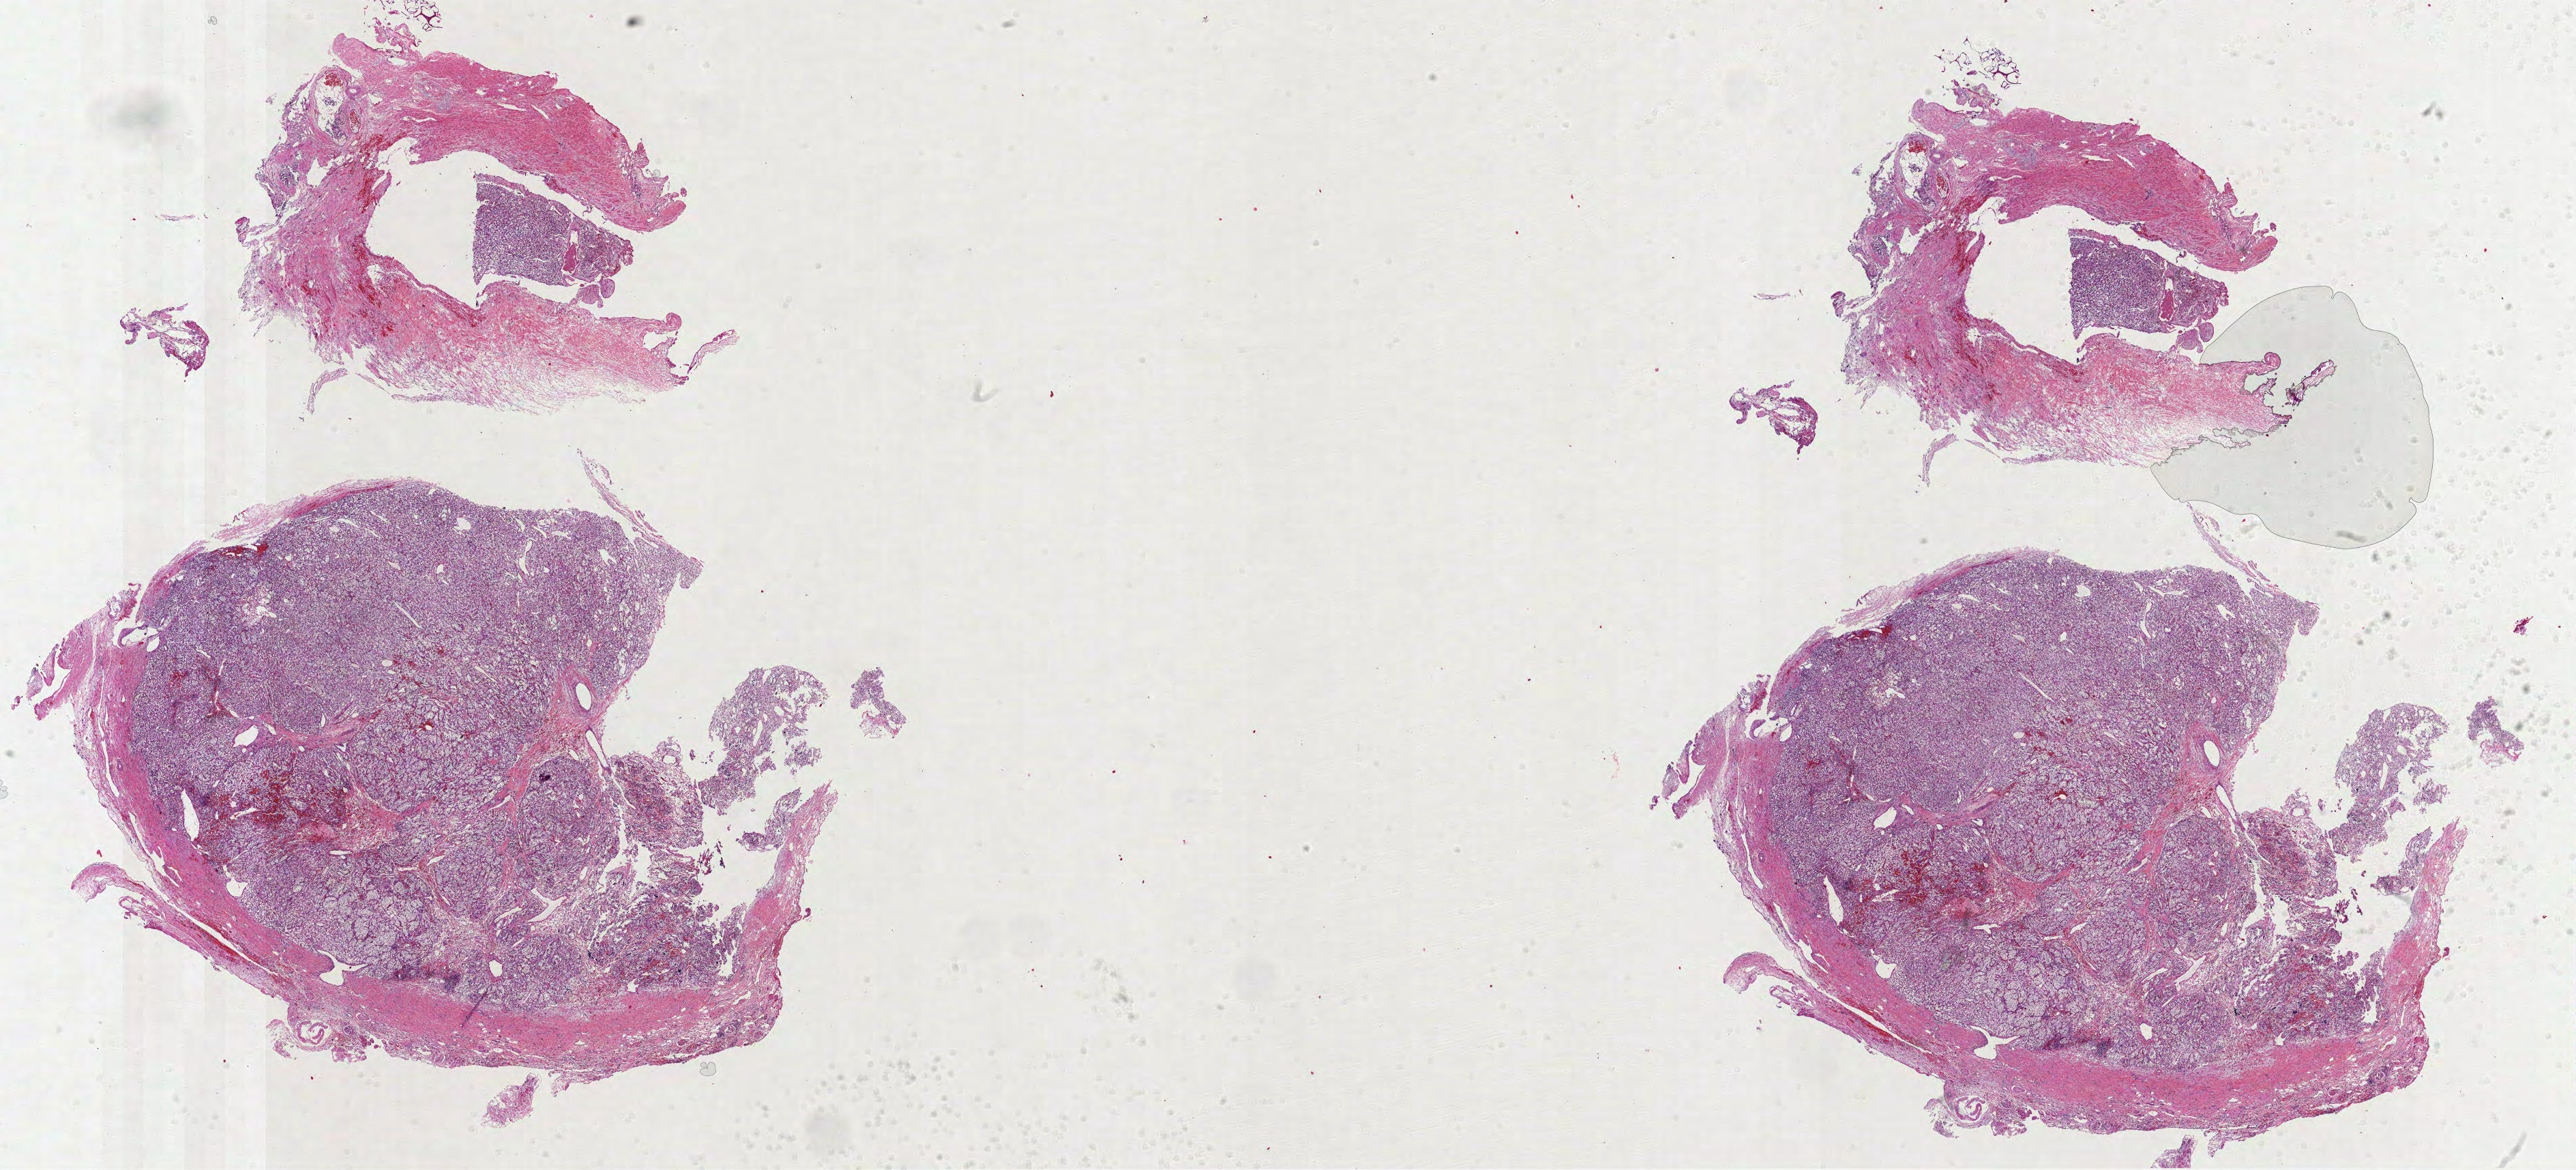
Whole-slide histology image, H&E-stained — shown as a low-resolution overview of the whole scanned area (about 30.5 x 13.8 mm, from a 40x scan). Formalin-fixed paraffin-embedded (FFPE) diagnostic section. Sample: primary tumour, kidney. Patient: male, age at initial diagnosis 59 years.
Histologic diagnosis: Clear cell adenocarcinoma, NOS.